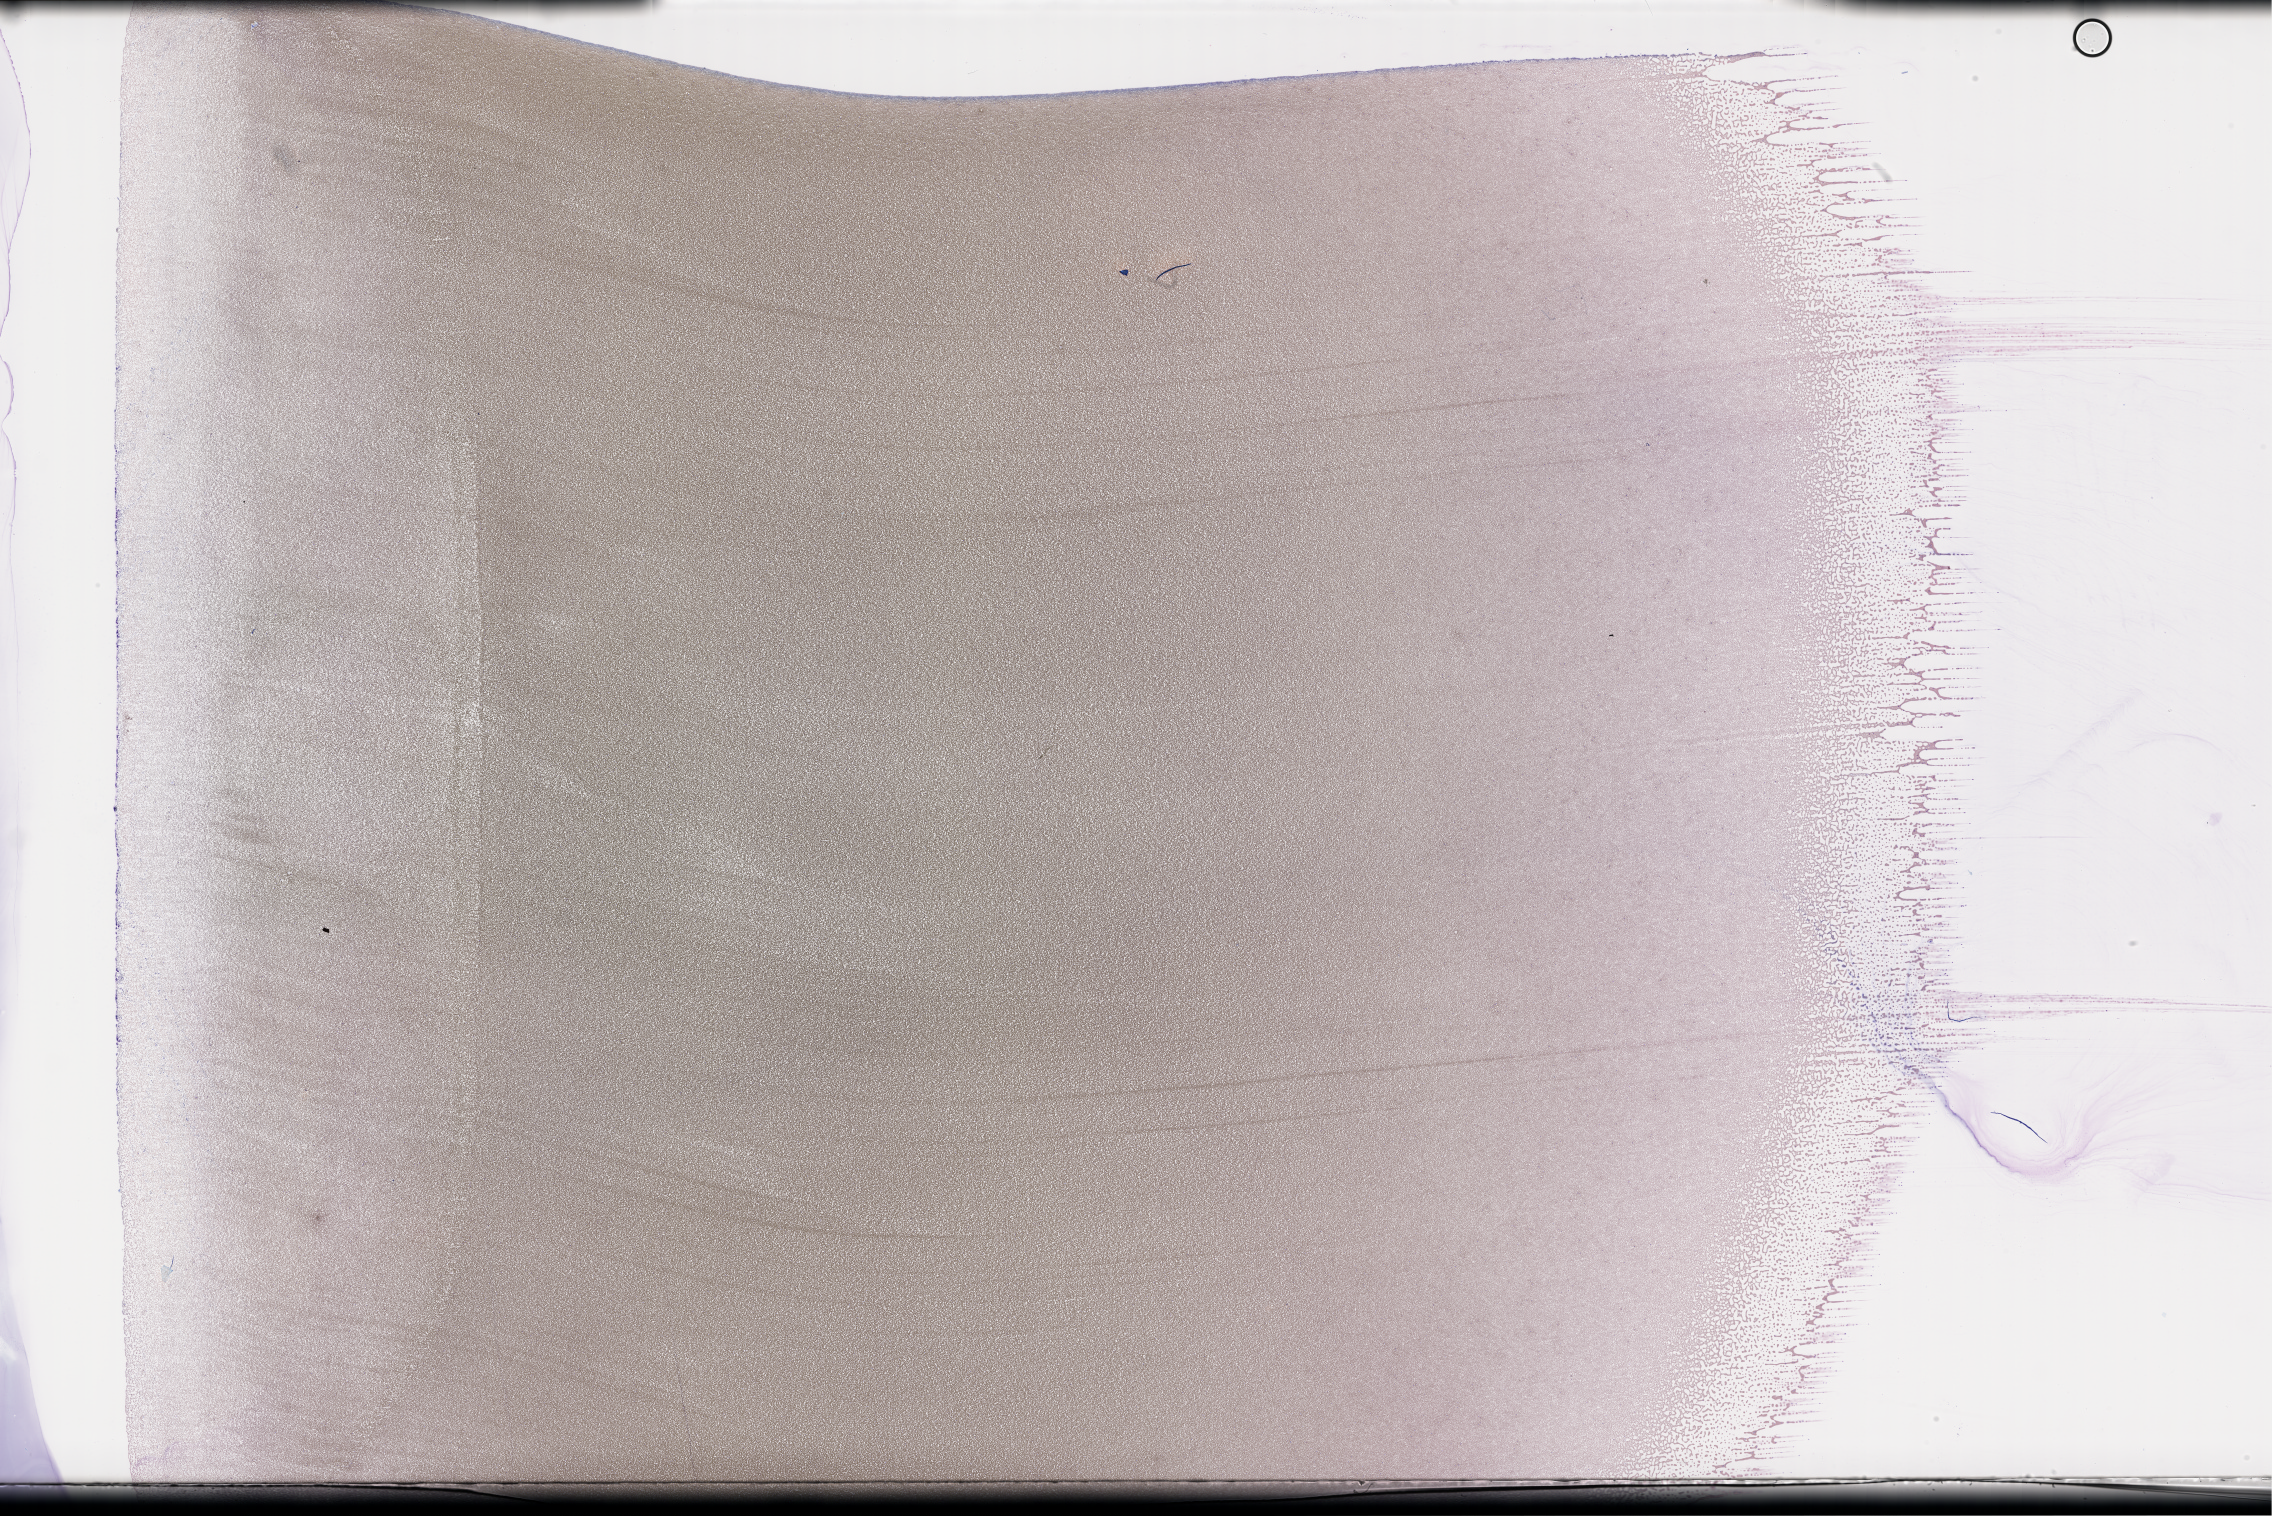
Wright–Giemsa-stained whole blood smear, whole-slide image, a low-resolution overview of the entire scanned area, about 36.7 x 24.5 mm, specimen time point: collected on treatment. Patient: male.
• patient diagnosis: Plasma Cell Myeloma